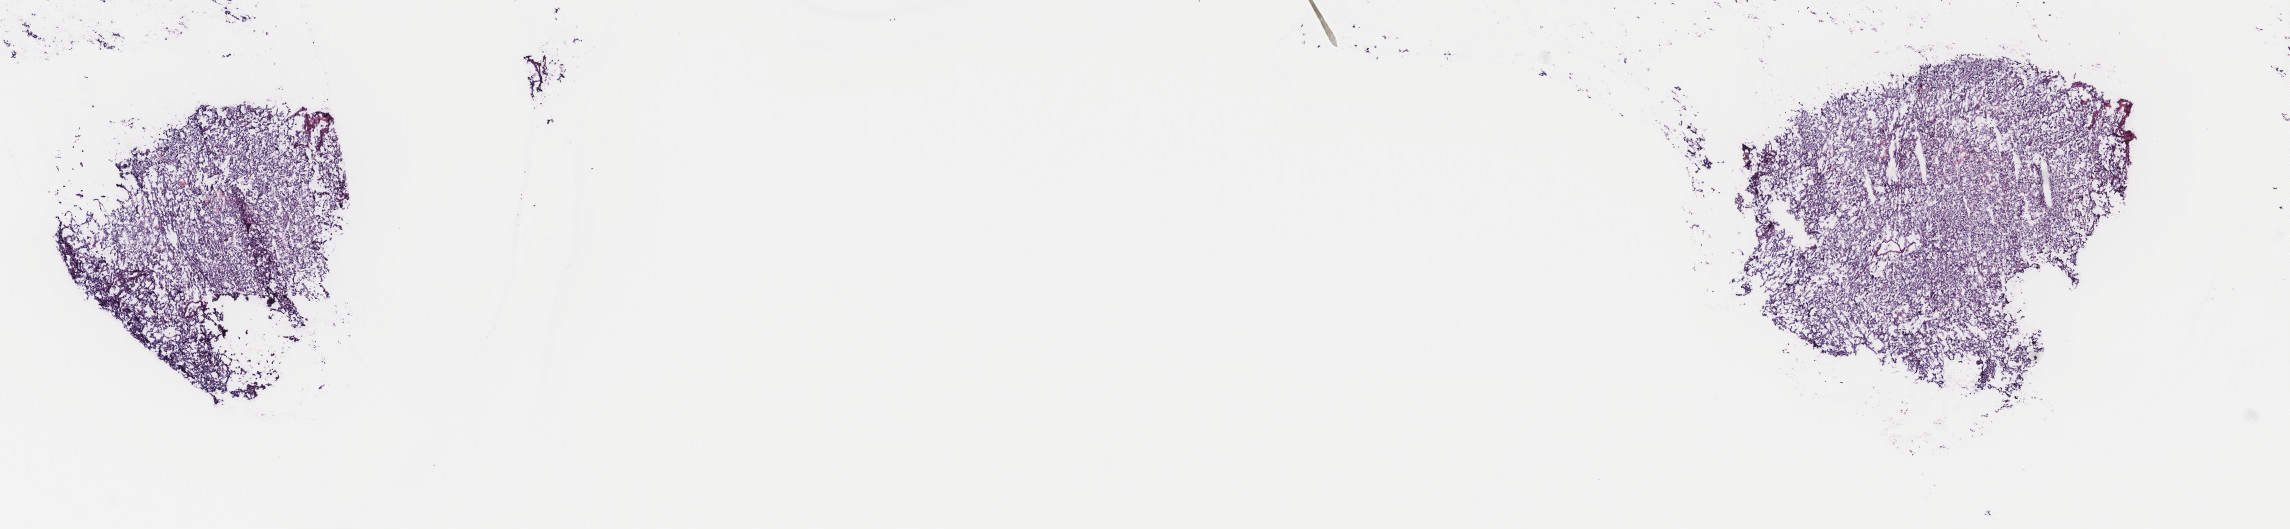
H&E-stained whole-slide image — shown as a low-resolution overview of the whole scanned area (about 18.2 x 4.2 mm). Frozen section from the top of the tissue portion. Primary tumour sample from the adrenal gland. Female patient; age at initial diagnosis 54 years. Pathologist review of this section (percent, as recorded): tumour cells 100%, tumour nuclei 95%, normal cells 0%, stromal cells 0%, necrosis 0%. Infiltration values recorded for this section: lymphocyte infiltration 0%, monocyte infiltration 0%, neutrophil infiltration 0%.
* histologic diagnosis: Pheochromocytoma, NOS